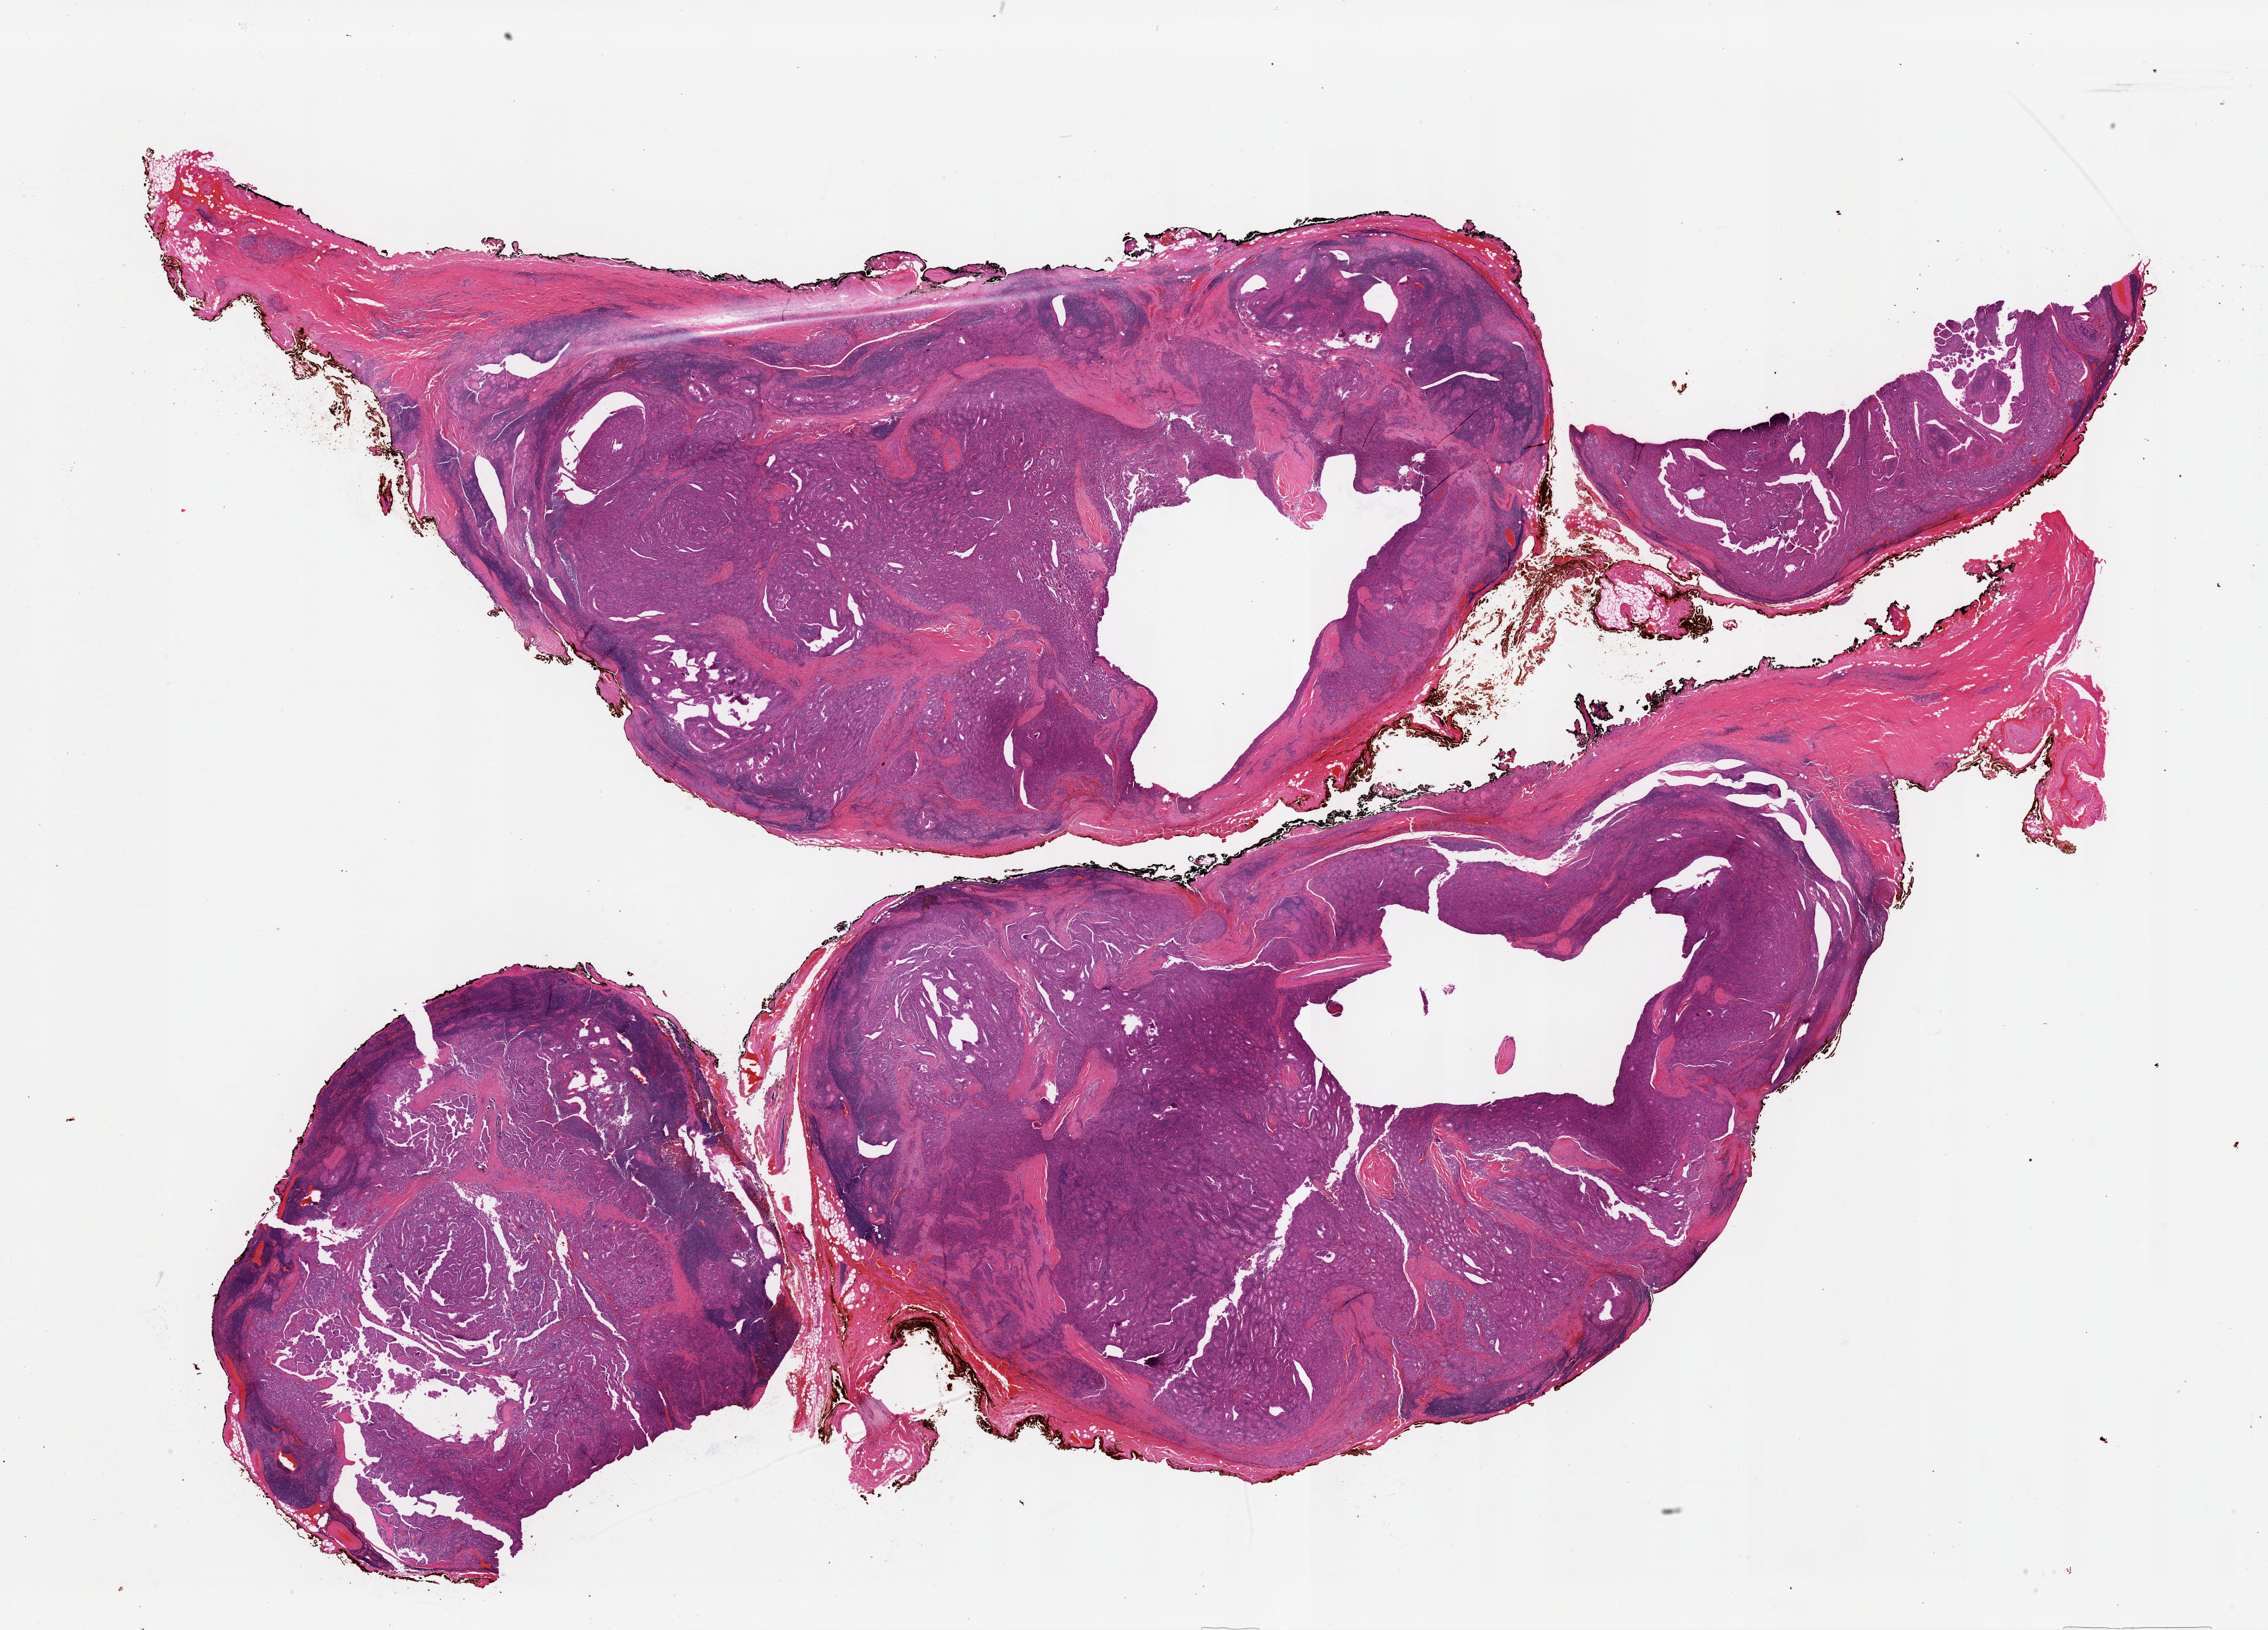
Hematoxylin and eosin (H&E) stained whole-slide image, shown as a low-resolution overview of the whole scanned area (about 31.7 x 22.8 mm, slide scanned at 40x), formalin-fixed paraffin-embedded (FFPE) diagnostic section, primary tumour sample from the thyroid. Patient: female, age at initial diagnosis 44 years.
Pathologic diagnosis: Papillary carcinoma, columnar cell. Laterality: left. Lymph nodes positive (case pathology): 2 of 10 examined. AJCC pathologic stage: I (7th edition).